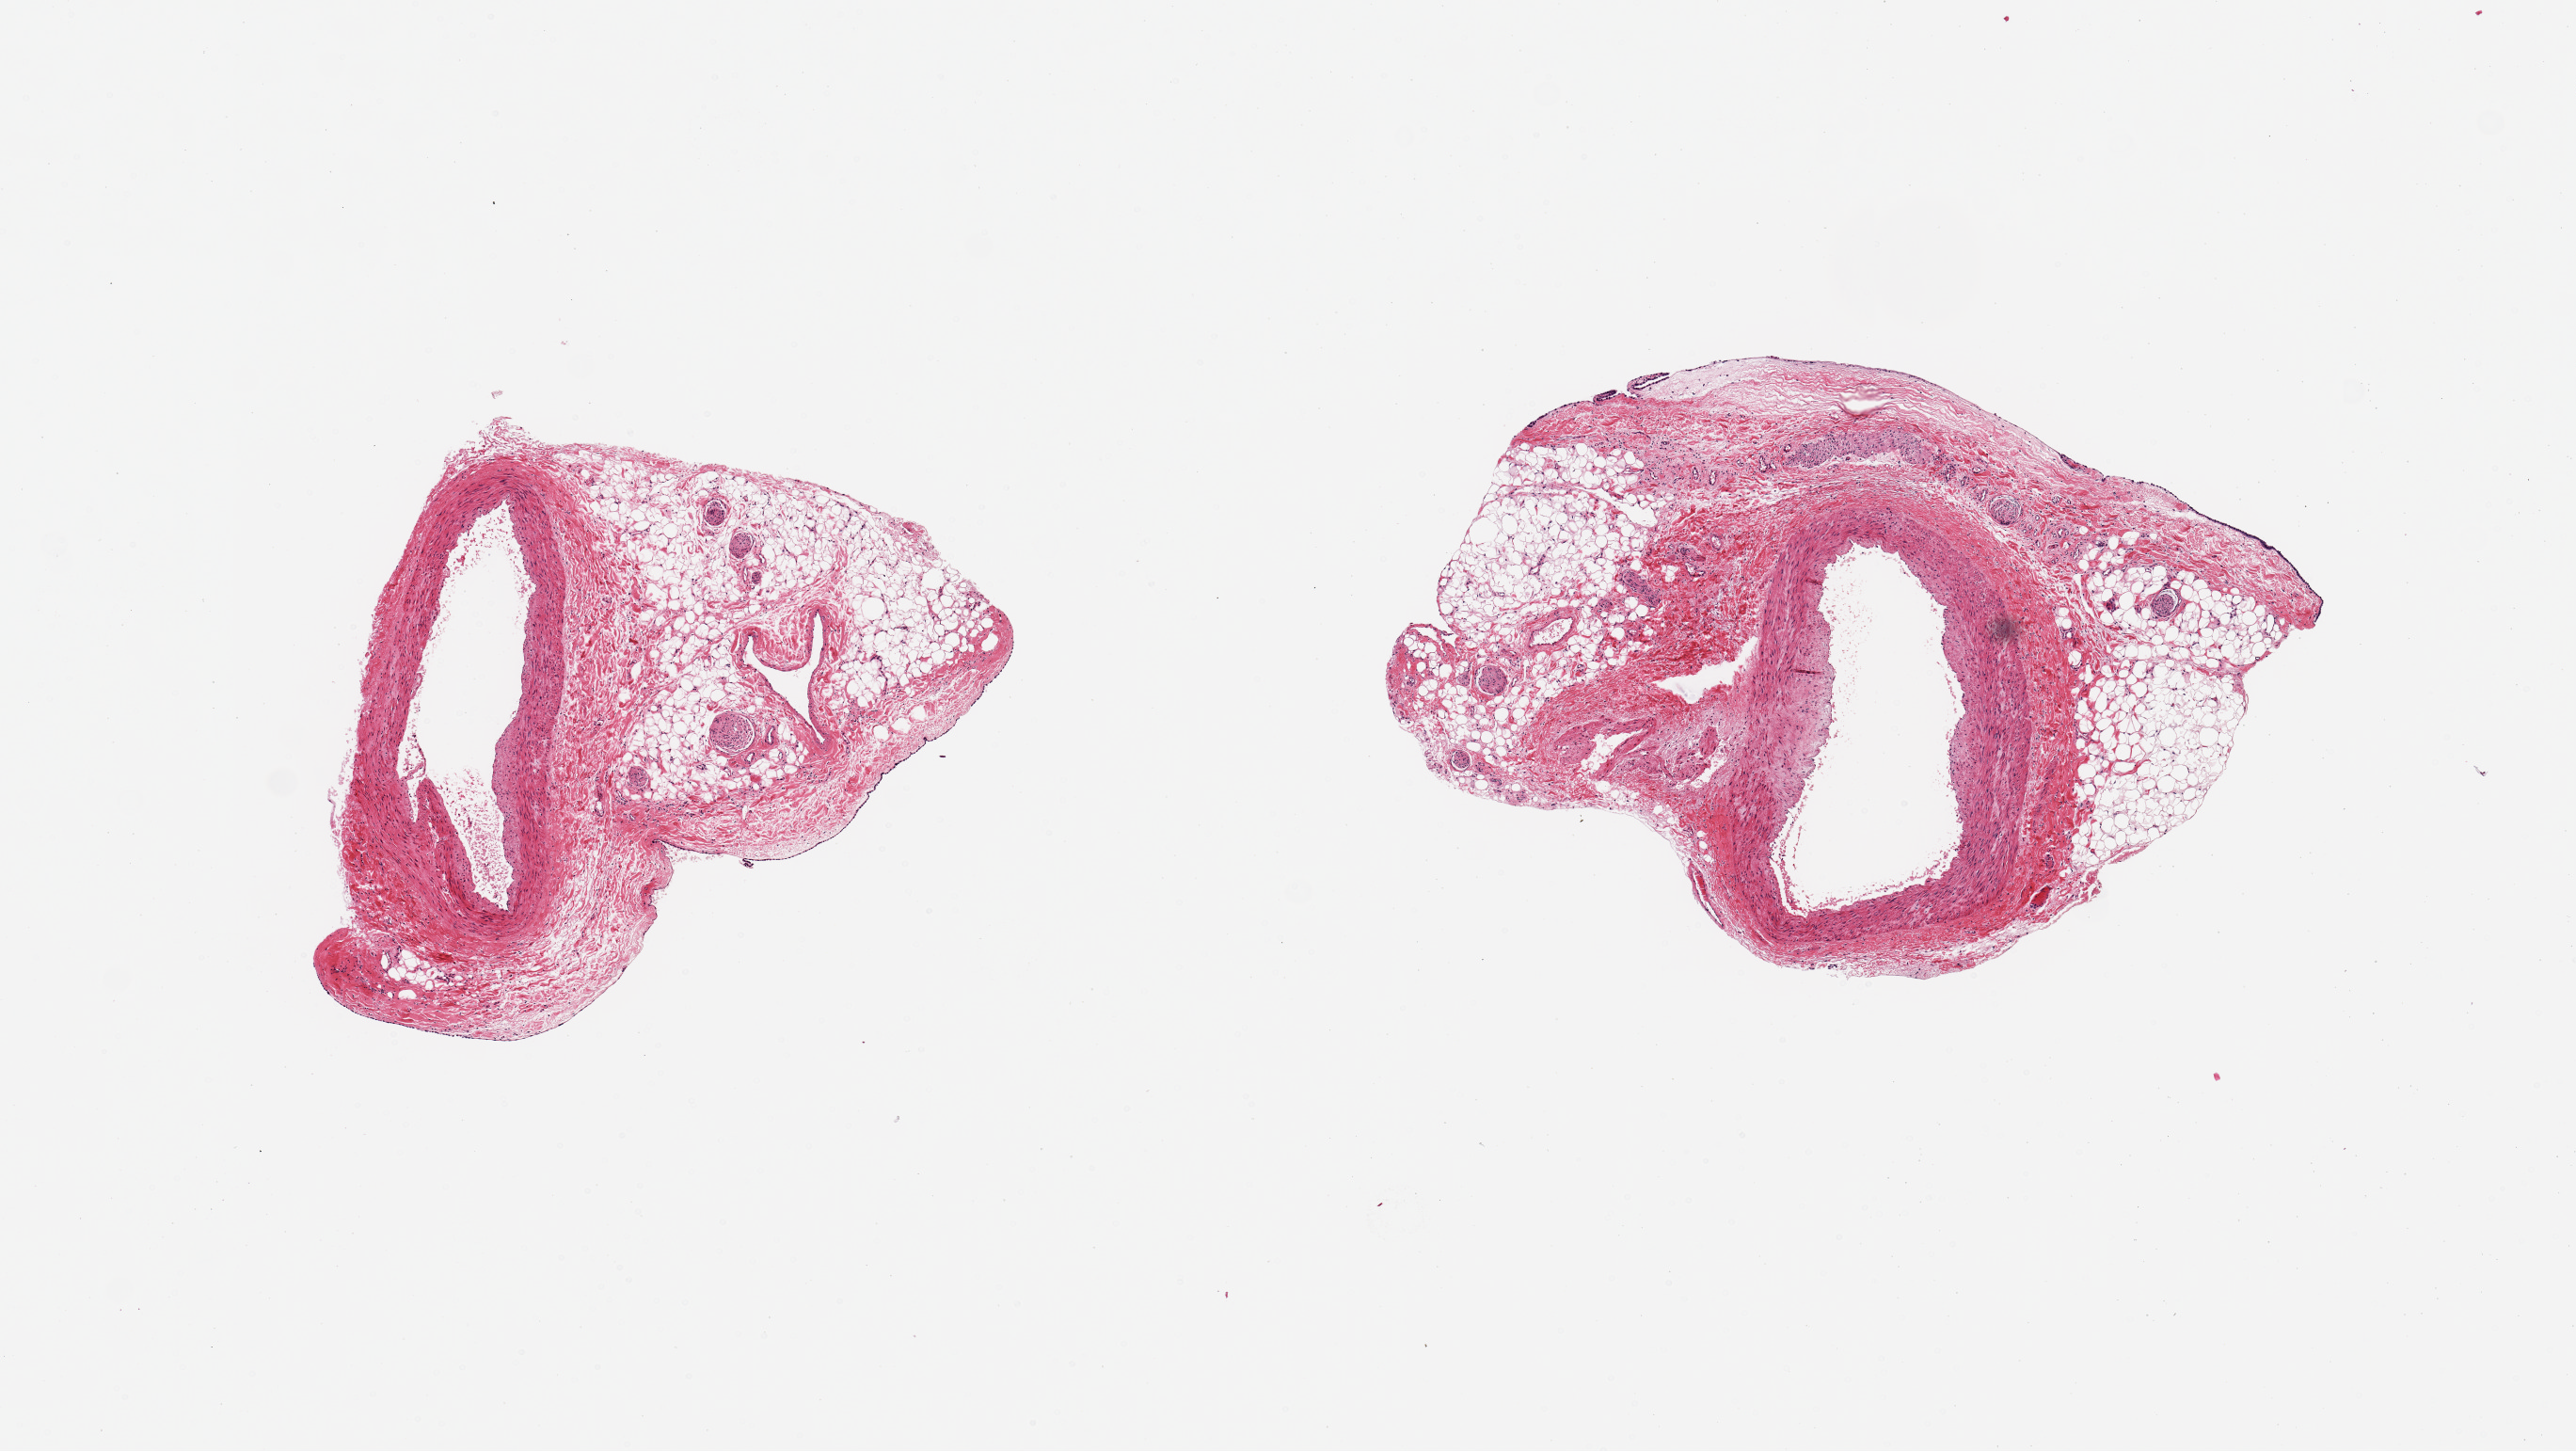
Whole-slide image, H&E stain, brightfield, whole scanned area (about 10.8 x 6.1 mm, from a 20x scan) shown as a low-resolution overview, PAXgene-fixed, paraffin-embedded tissue, section of coronary artery (target tissue), tissue donor sample. Donor: male.
Reviewer comment on this tissue sample: 2 pieces each with 2 mm artery; small plaque.